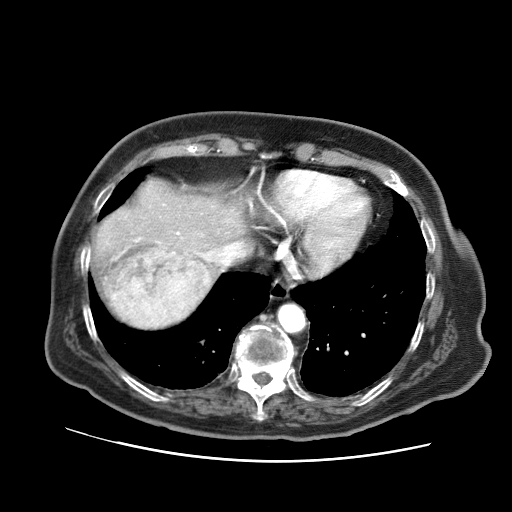
Contrast-enhanced abdominal CT (liver protocol), one axial slice. 120 kVp. Soft-tissue window (W 400 / L 40 HU). 512 × 512 image matrix, field of view 380 × 380 mm. From the clinical record (not read from this slice): diagnosis: hepatocellular carcinoma (patient treated with transarterial chemoembolisation; whether this scan precedes or follows treatment is not stated here); TNM stage (as recorded): Stage-I; Child-Pugh class: A; tumour differentiation: well differentiated; tumour nodularity: uninodular.
Structures marked on this image (semi-automatically segmented with operator editing):
- abdominal aorta: box from (x=279, y=304) to (x=304, y=332) px
- liver parenchyma outside the tumour (the mass and vessels are separate outlines, so this box may not span the whole liver): (x=90, y=180)–(x=246, y=328)
- mass: (x=104, y=242)–(x=210, y=328)
- liver vessels: (x=135, y=232)–(x=215, y=261)